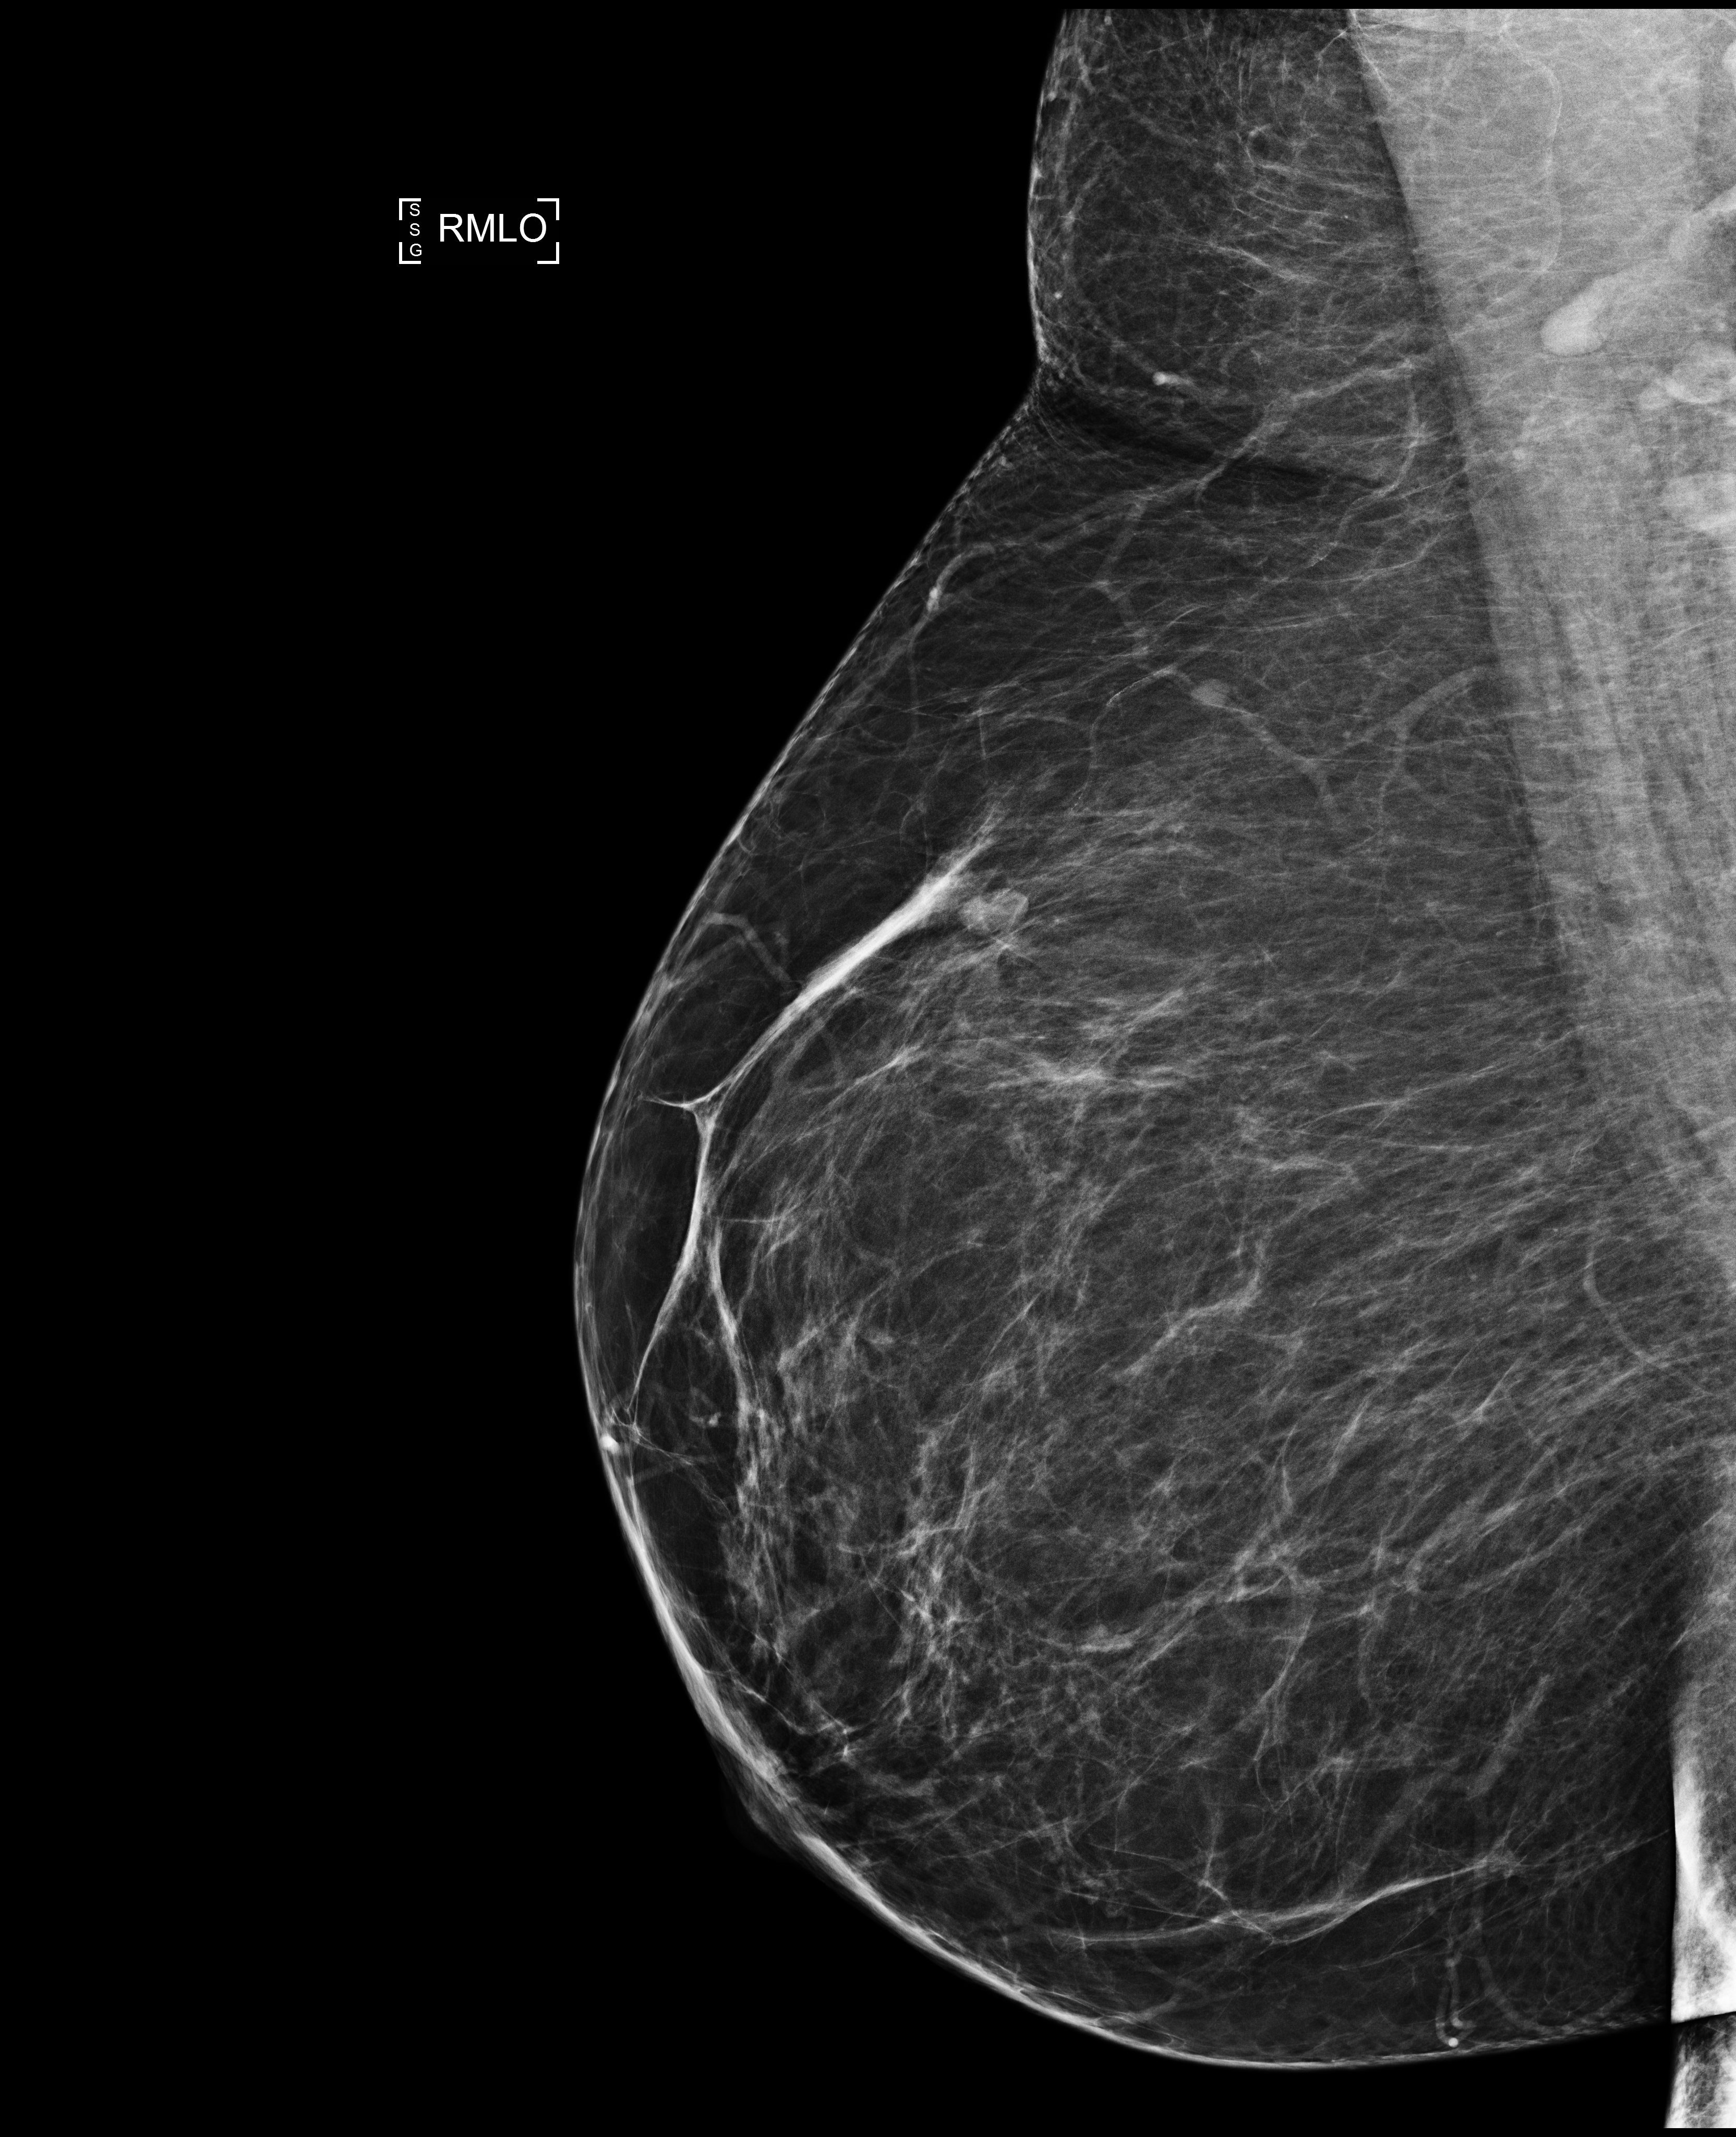
Annual screening mammography examination, system: Selenia Dimensions. Patient aged 51 years (female).
Image type: full-field digital mammogram. Breast: right. Projection: medio-lateral oblique projection.